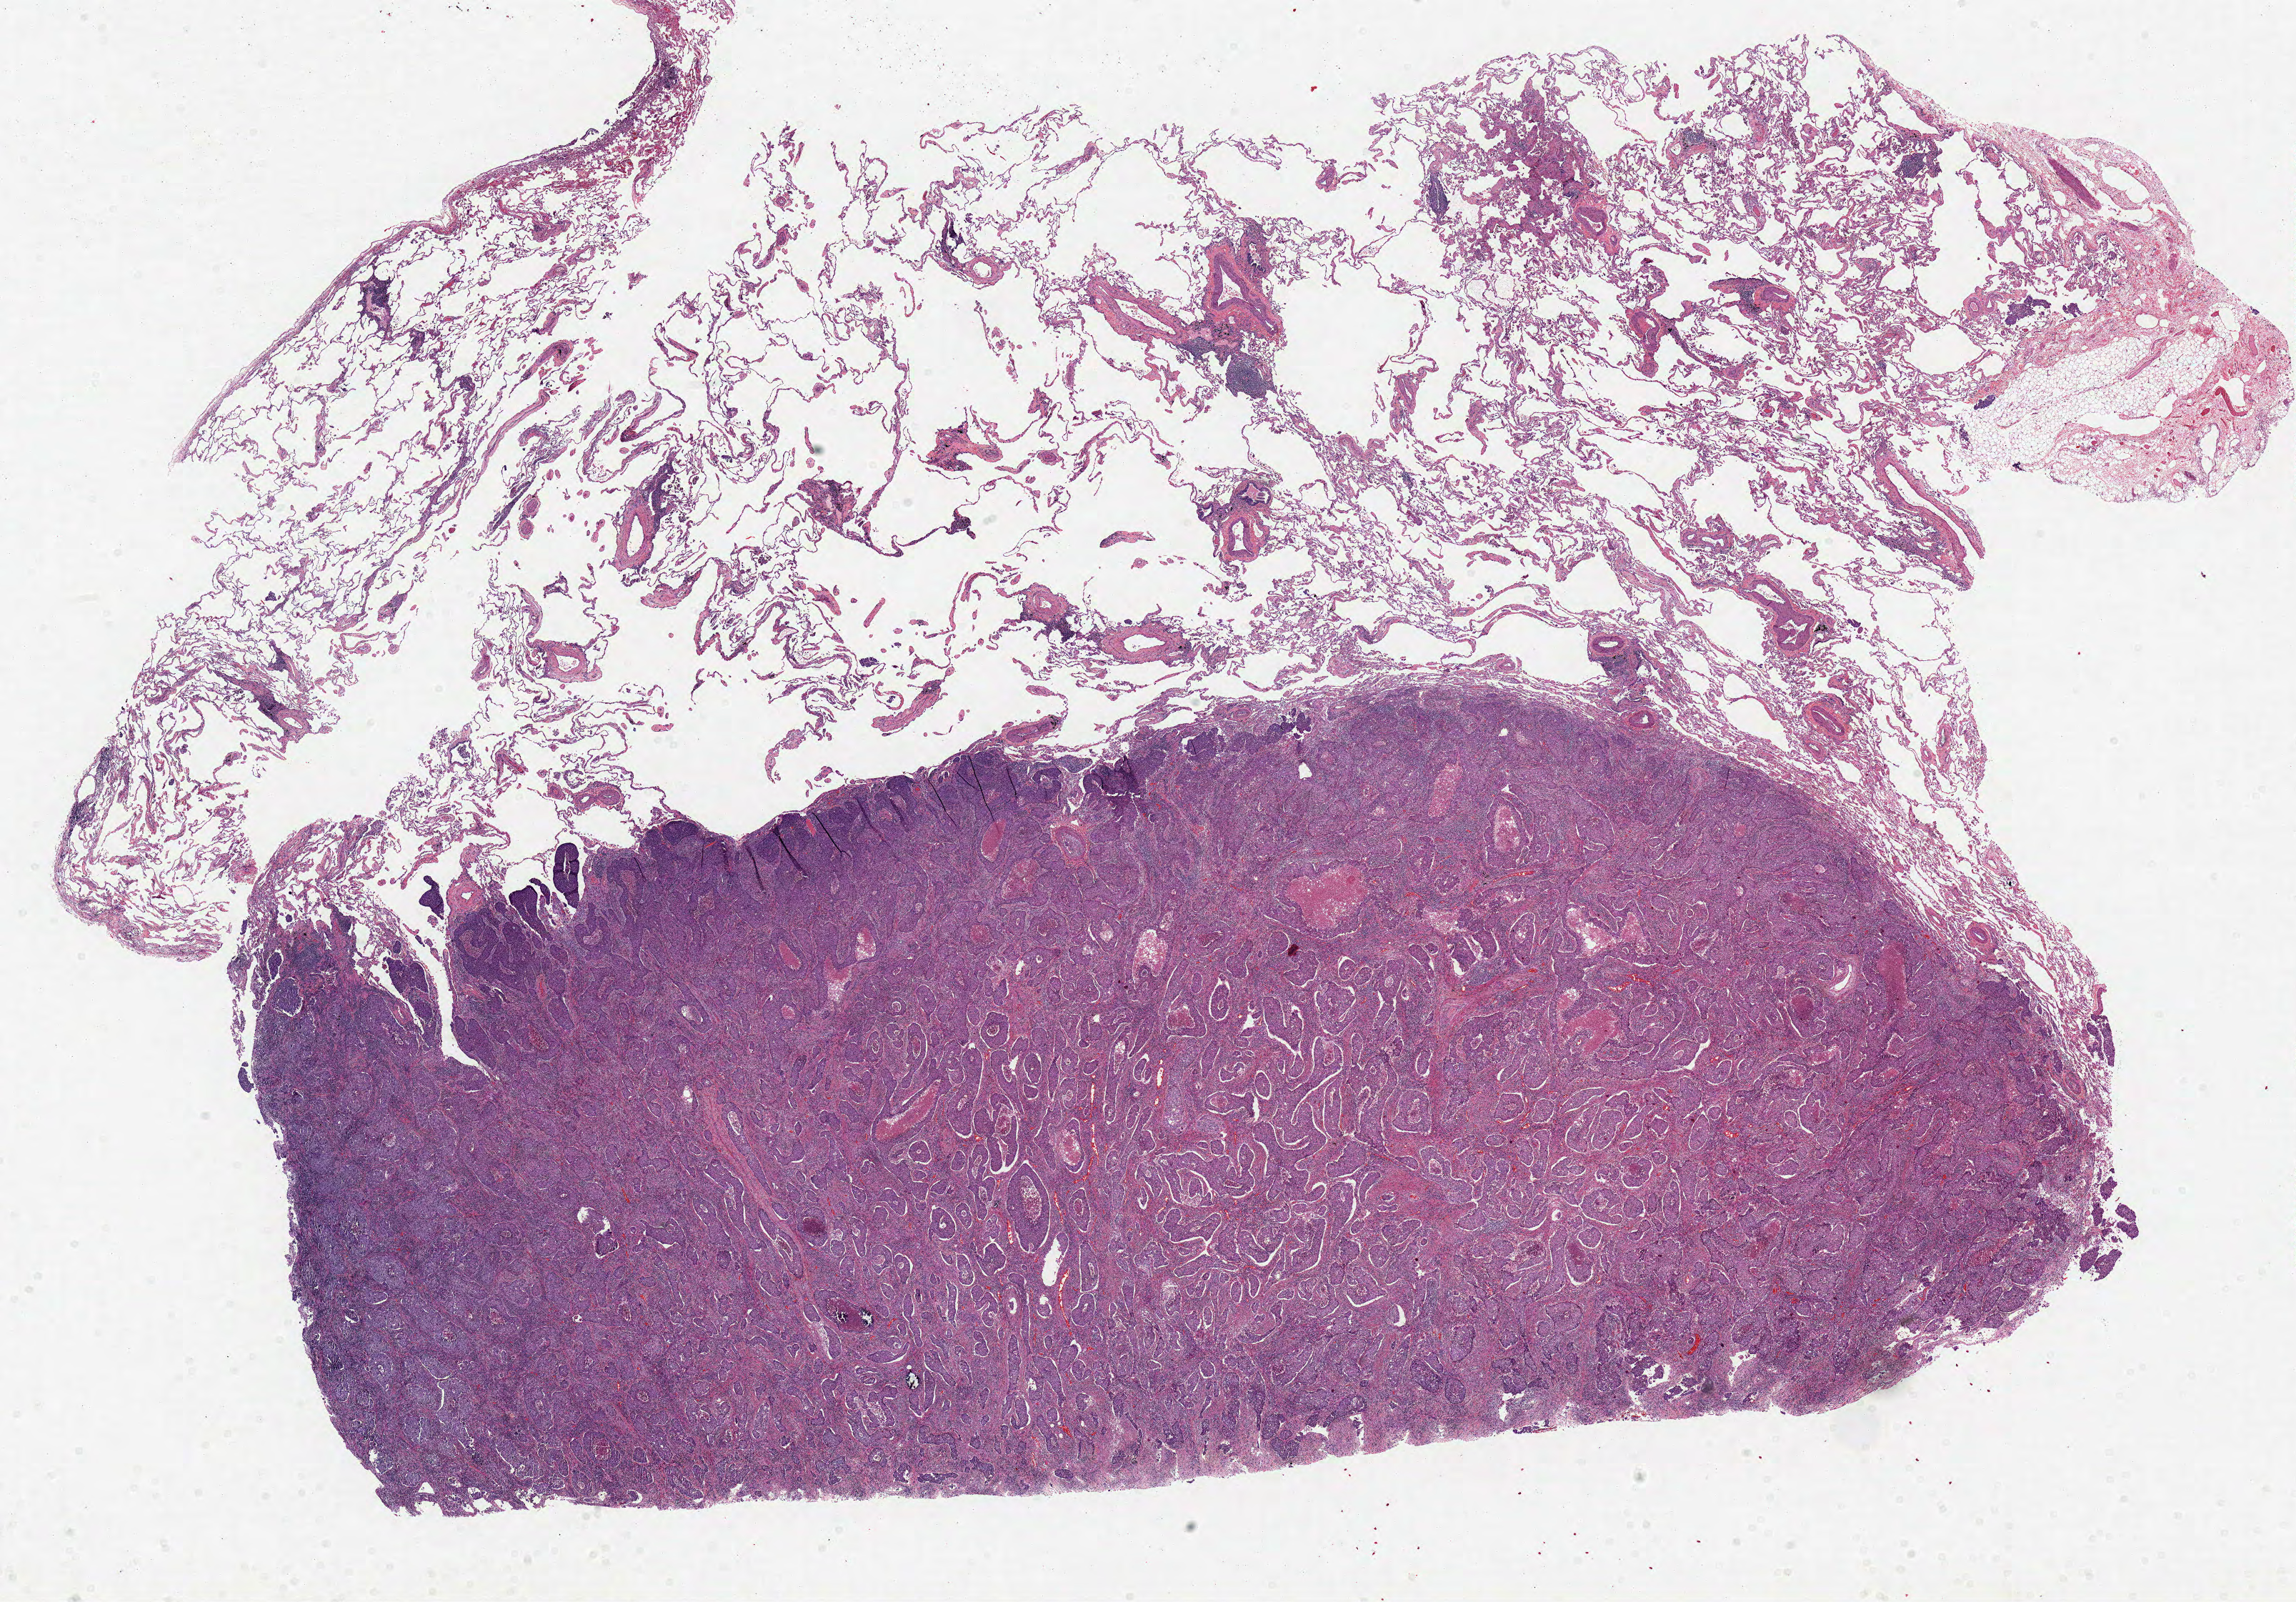
H&E whole-slide image, a low-resolution overview of the entire scanned area, about 25.9 x 18.1 mm (slide scanned at 20x), formalin-fixed paraffin-embedded (FFPE) diagnostic section, sample: primary tumour, lung. Patient: female, age at initial diagnosis 73 years.
TNM: T3 N0 M0. AJCC pathologic stage: IIB. Histologic diagnosis: Squamous cell carcinoma, NOS (upper lobe, lung).